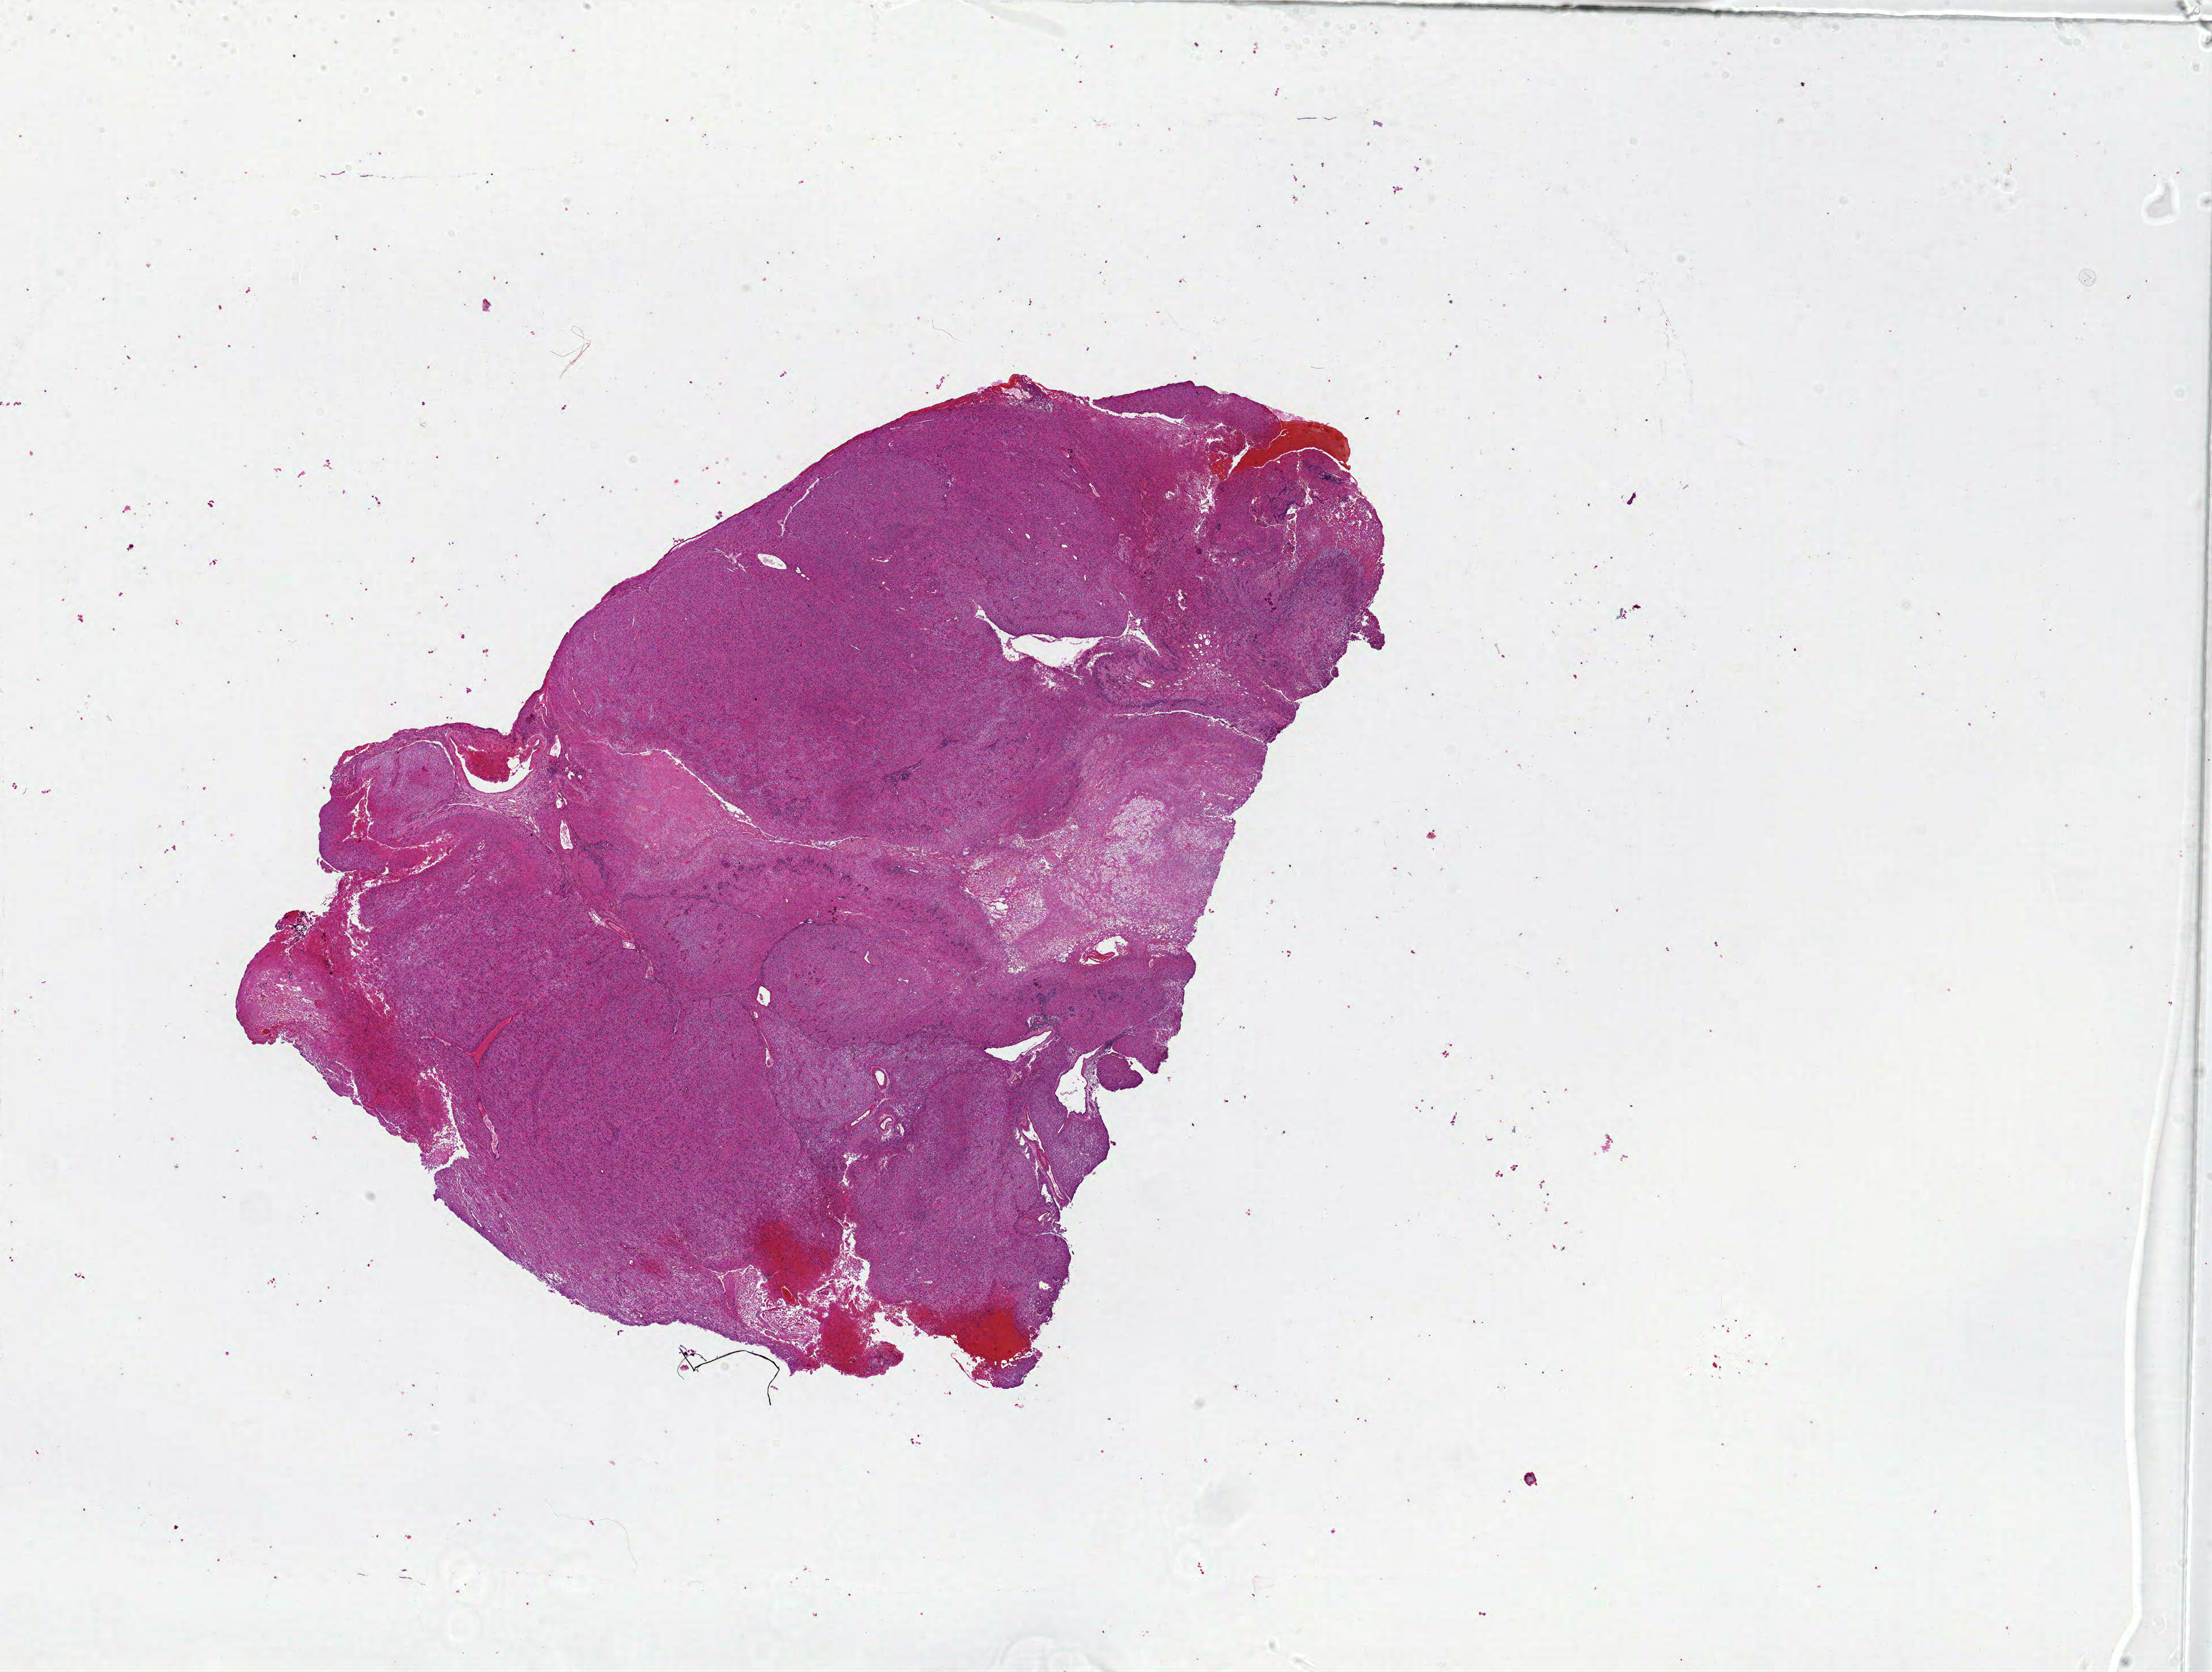
Digitized Hematoxylin and eosin (H&E) stained tissue section (whole slide) — whole scanned area (about 31.0 x 23.4 mm, slide scanned at 20x) shown as a low-resolution overview, formalin-fixed paraffin-embedded (FFPE) diagnostic section, sample: primary tumour, brain. Male, age 57 years at initial diagnosis.
Histologic diagnosis: Glioblastoma.